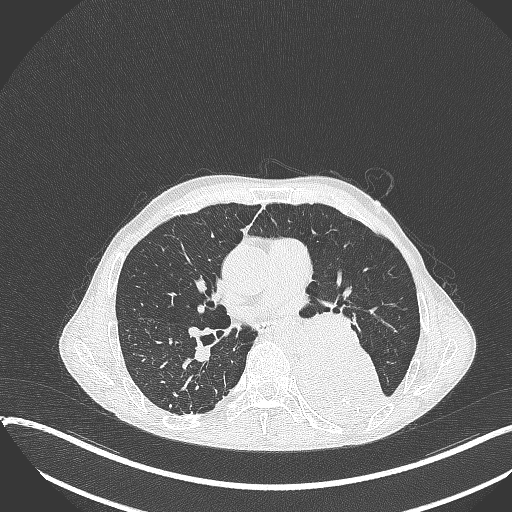
Chest CT, one axial slice. Position 198 of 401 along the scan axis. Reconstruction kernel B70f. Lung window (W 1500 / L -600 HU). 512 × 512 image matrix, field of view 400 × 400 mm. Male patient, age 57 years. From the clinical record (not read from this slice): clinical TNM (as recorded): T4 N0 M0.
Annotated regions visible in this slice (rectangle marked by the reading radiologist):
- lung tumour (recorded histology: squamous cell carcinoma): bounding box [x1, y1, x2, y2] px = [289, 328, 387, 427]